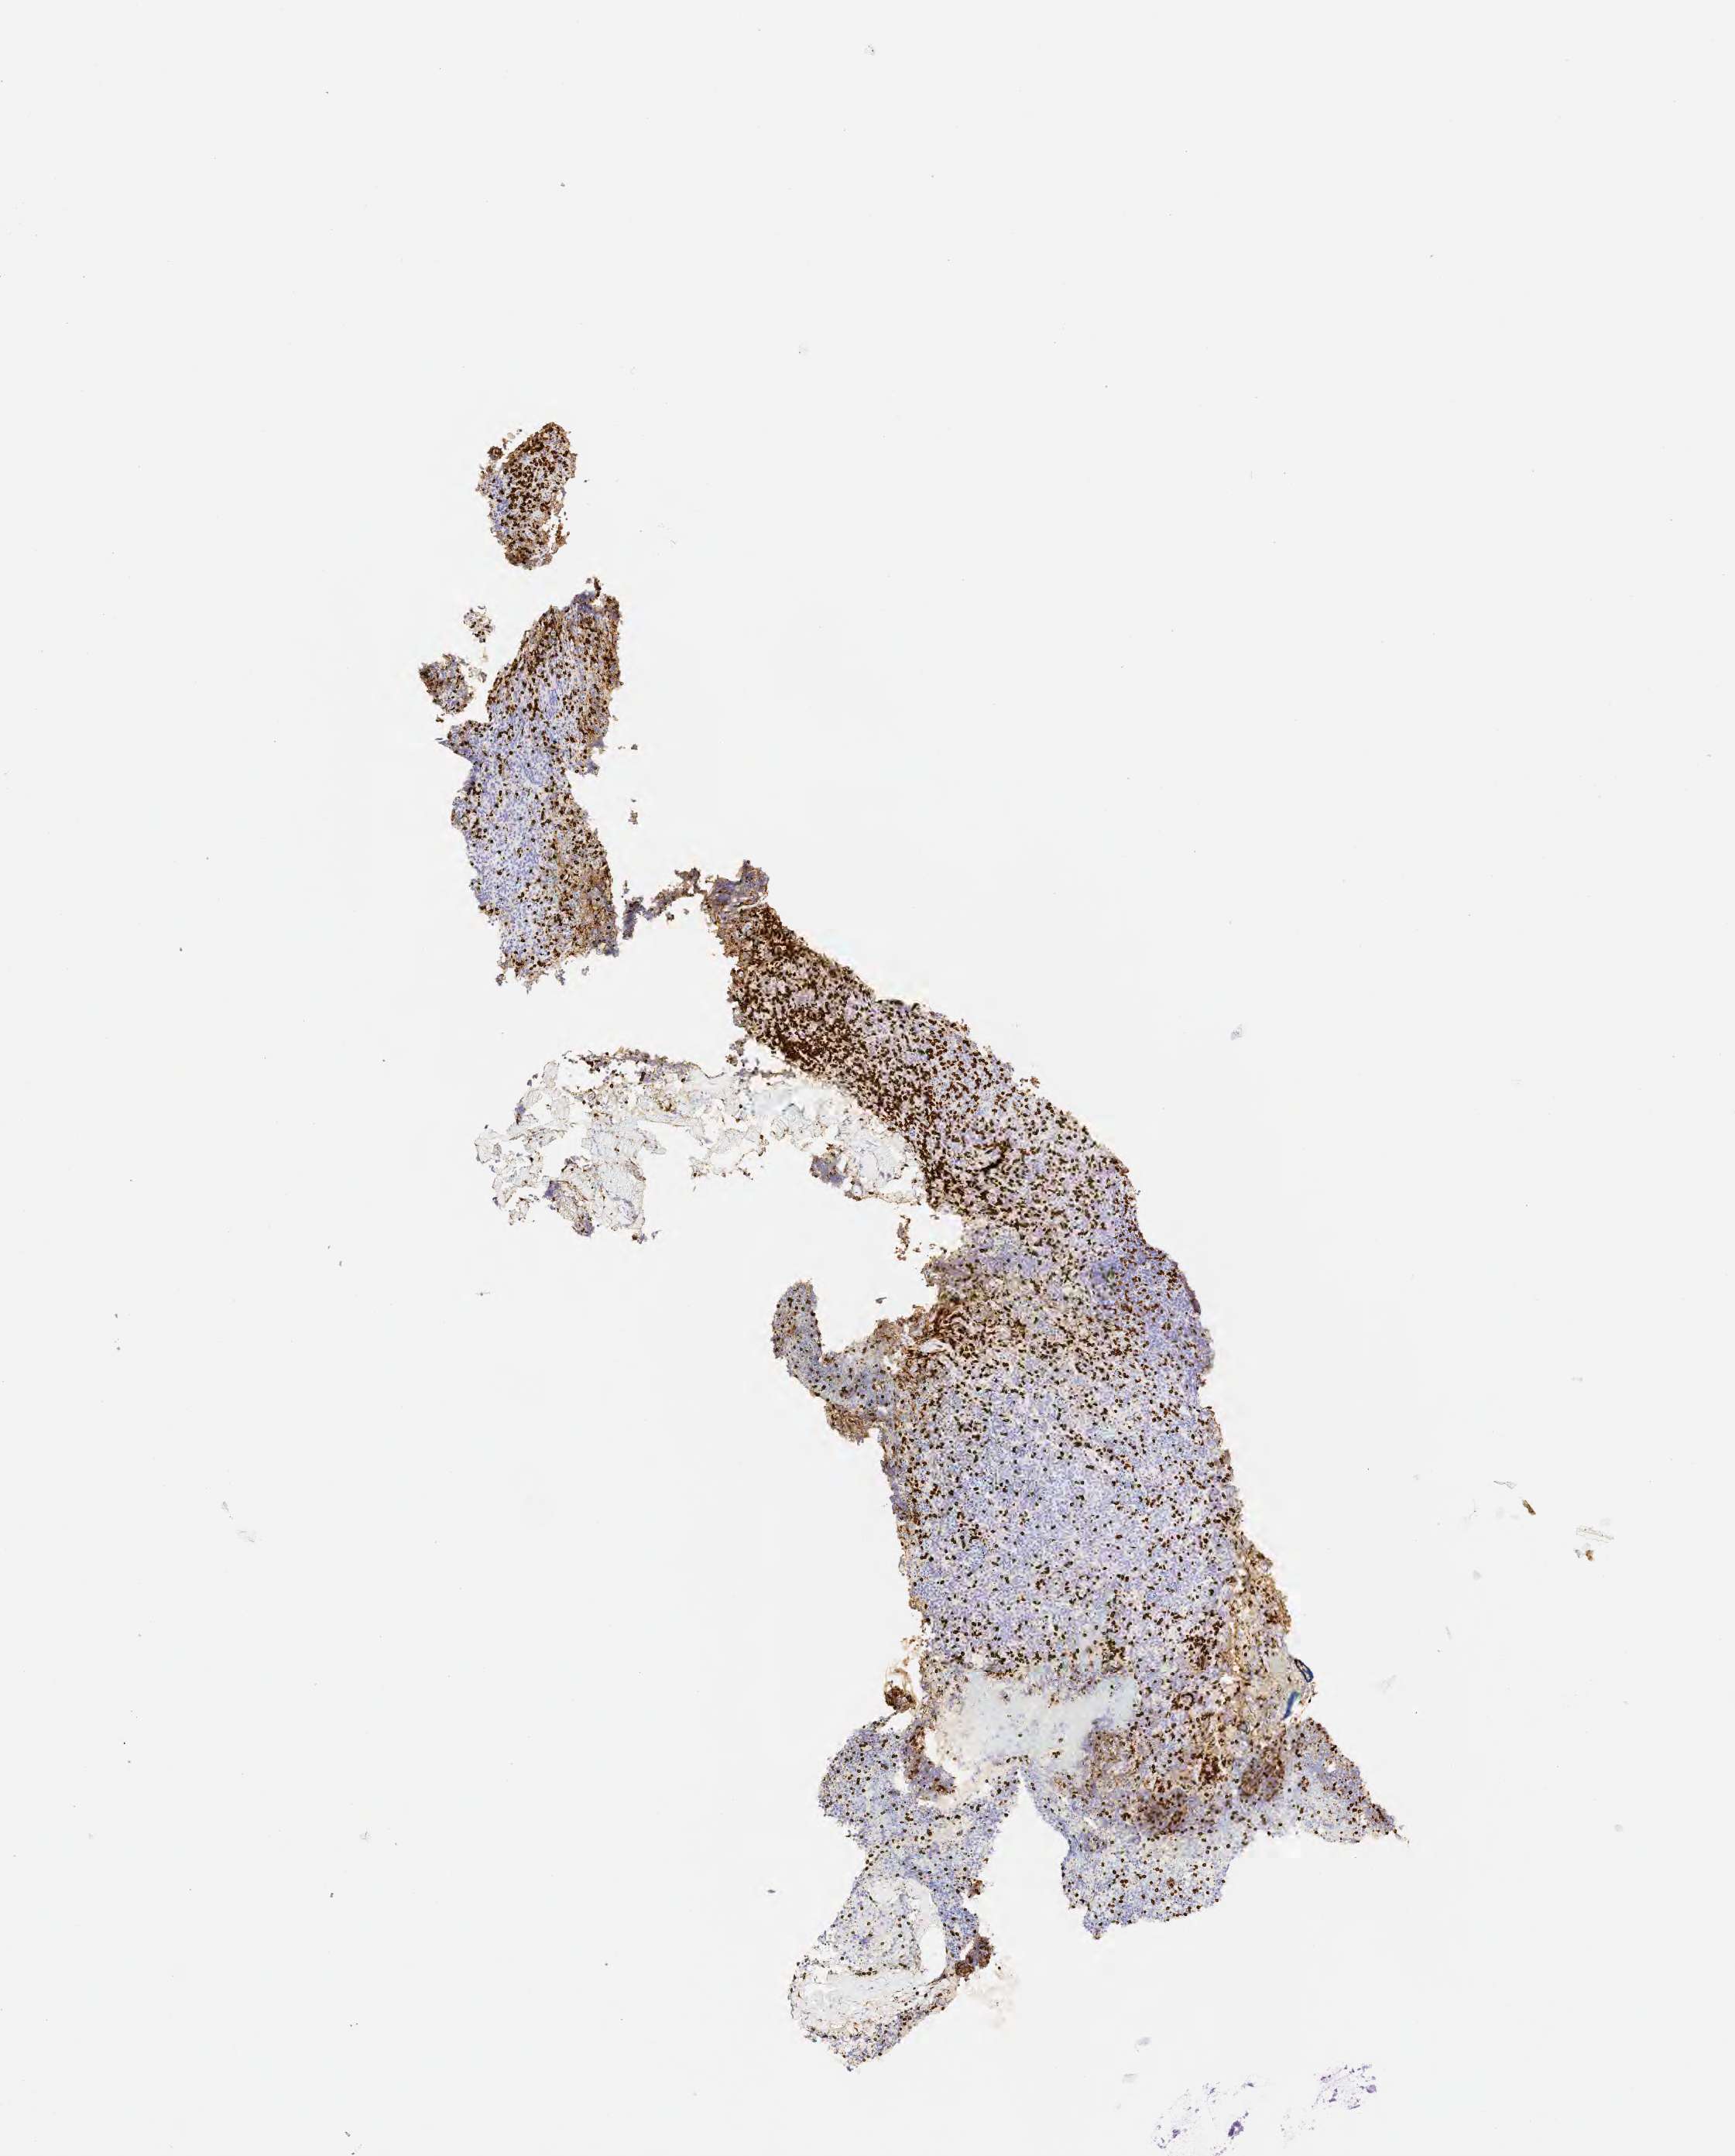
IHC for CD3, whole-slide image, low-resolution overview of the scanned area, about 4.5 x 5.6 mm, specimen: tumor tissue. Female patient, age 27 years.
Histologic diagnosis: Diffuse large B-cell lymphoma, NOS.